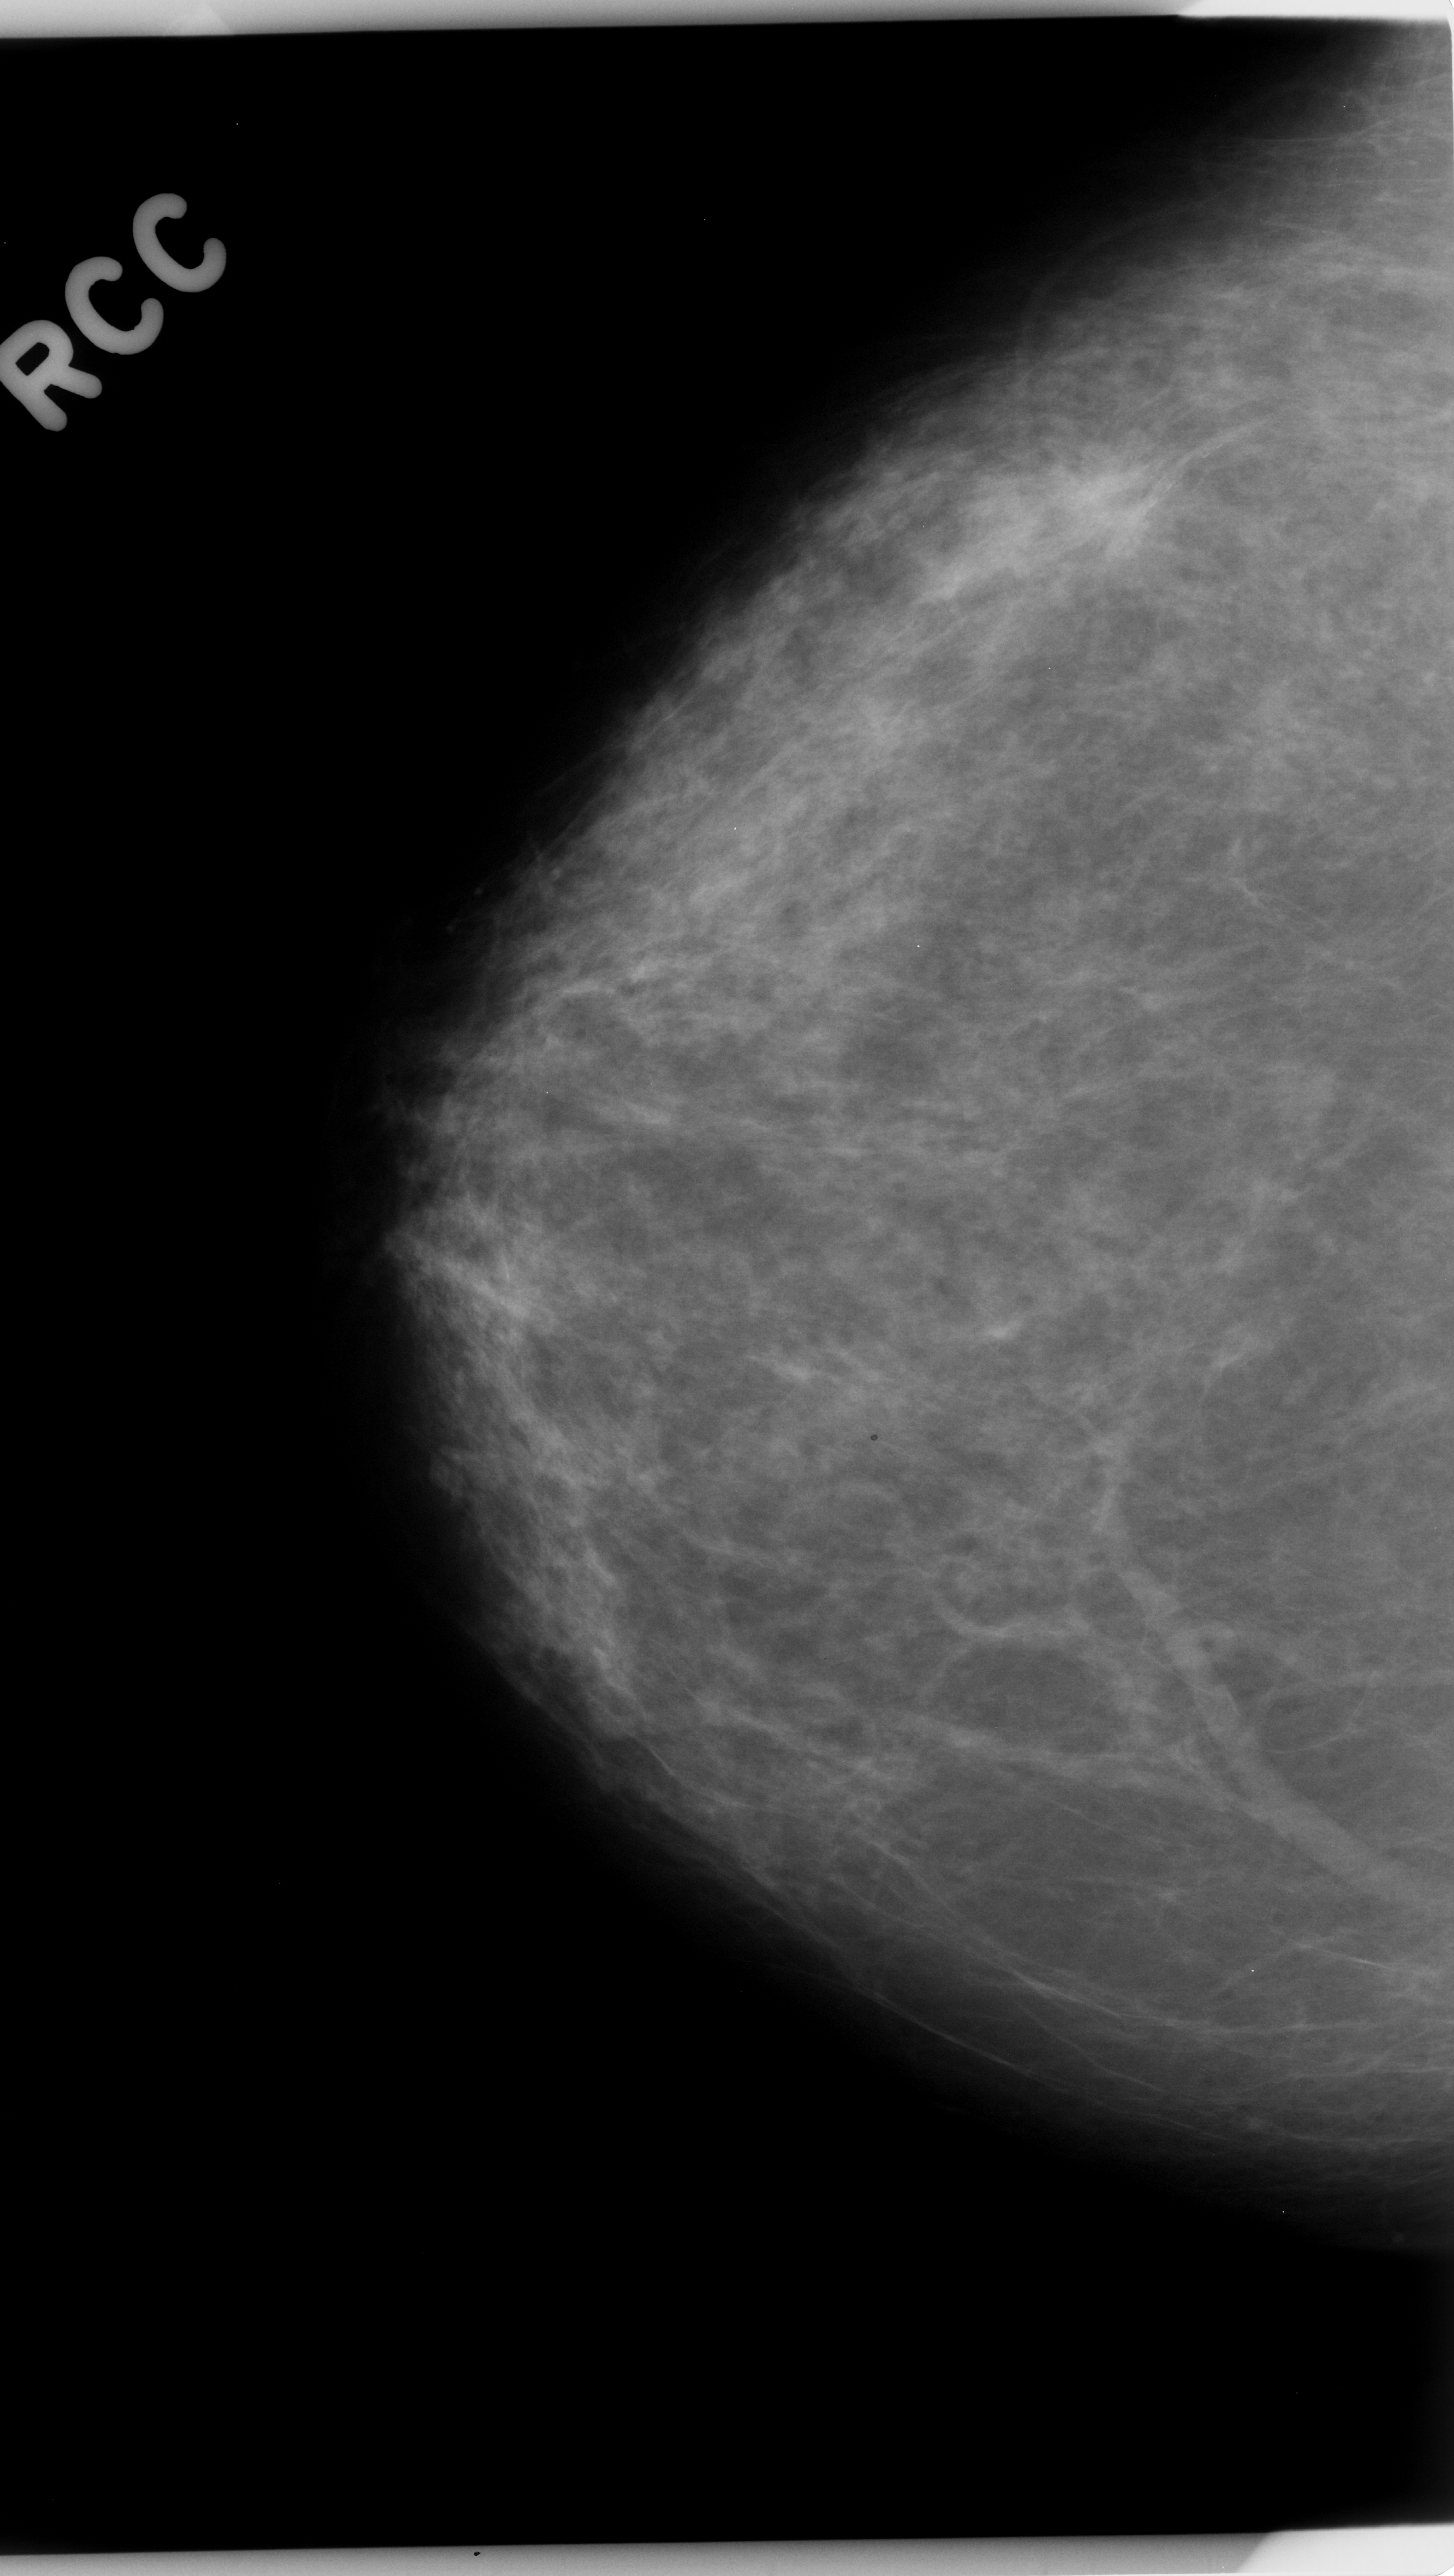
Scanned film-screen mammogram; right breast; craniocaudal (CC) view; BI-RADS breast density category 2 (scale 1–4); 1454 × 2576 image matrix.
Marked abnormalities (boxes around the expert regions of interest):
- mass, shape irregular, margins spiculated; BI-RADS assessment category 5; pathology (as recorded): malignant: box from (x=953, y=419) to (x=1170, y=608) px